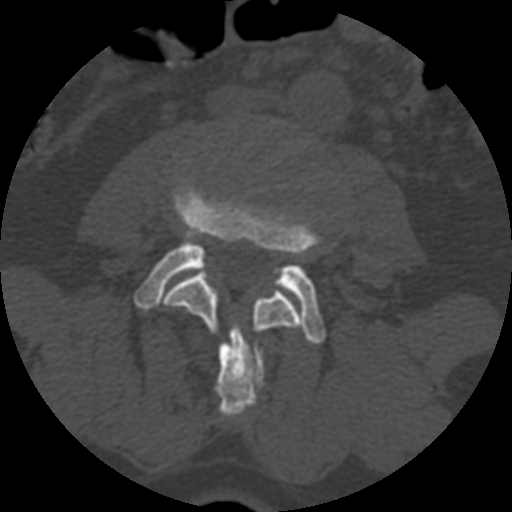
CT including the spine, one axial slice; position 293 of 399 along the scan axis; reconstruction kernel STANDARD; bone window (W 1800 / L 400 HU); 1.25 mm slice thickness; 512 × 512 image matrix, field of view 160 × 160 mm. Patient age 71 years. Case-level facts recorded for this patient, not image findings: primary cancer: prostate.
Outlined on this slice (semi-automatic segmentation, software-assisted and operator-edited):
- L3 vertebra: bounding box <163,269,302,415> (left, top, right, bottom; pixels)
- L4 vertebra: <135,179,325,343>